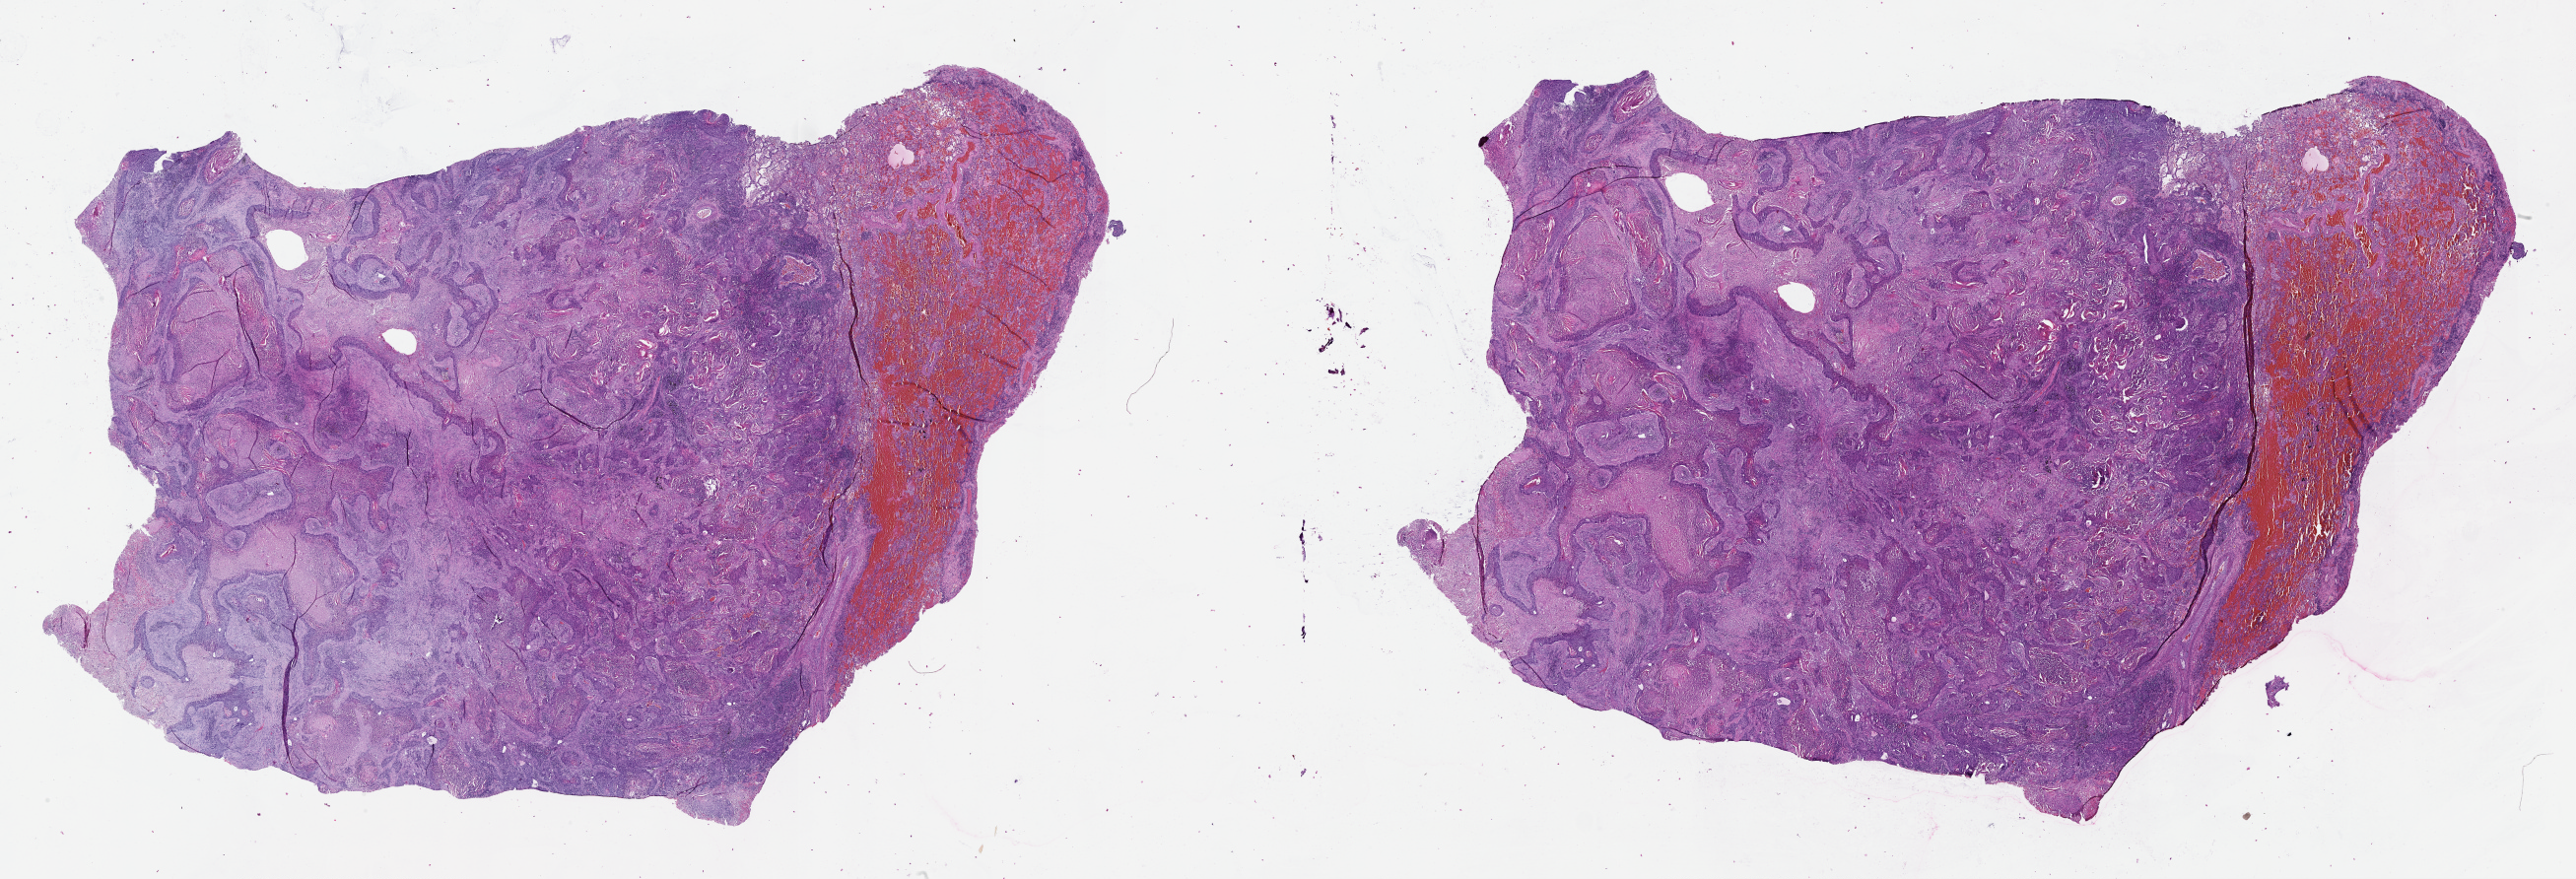
Hematoxylin and eosin (H&E) stained whole-slide image, whole scanned area (about 42.1 x 14.4 mm) shown as a low-resolution overview; tumour tissue sample, lung. Male, 49 y/o.
* patient diagnosis (cohort enrolment): squamous cell carcinoma (lung)